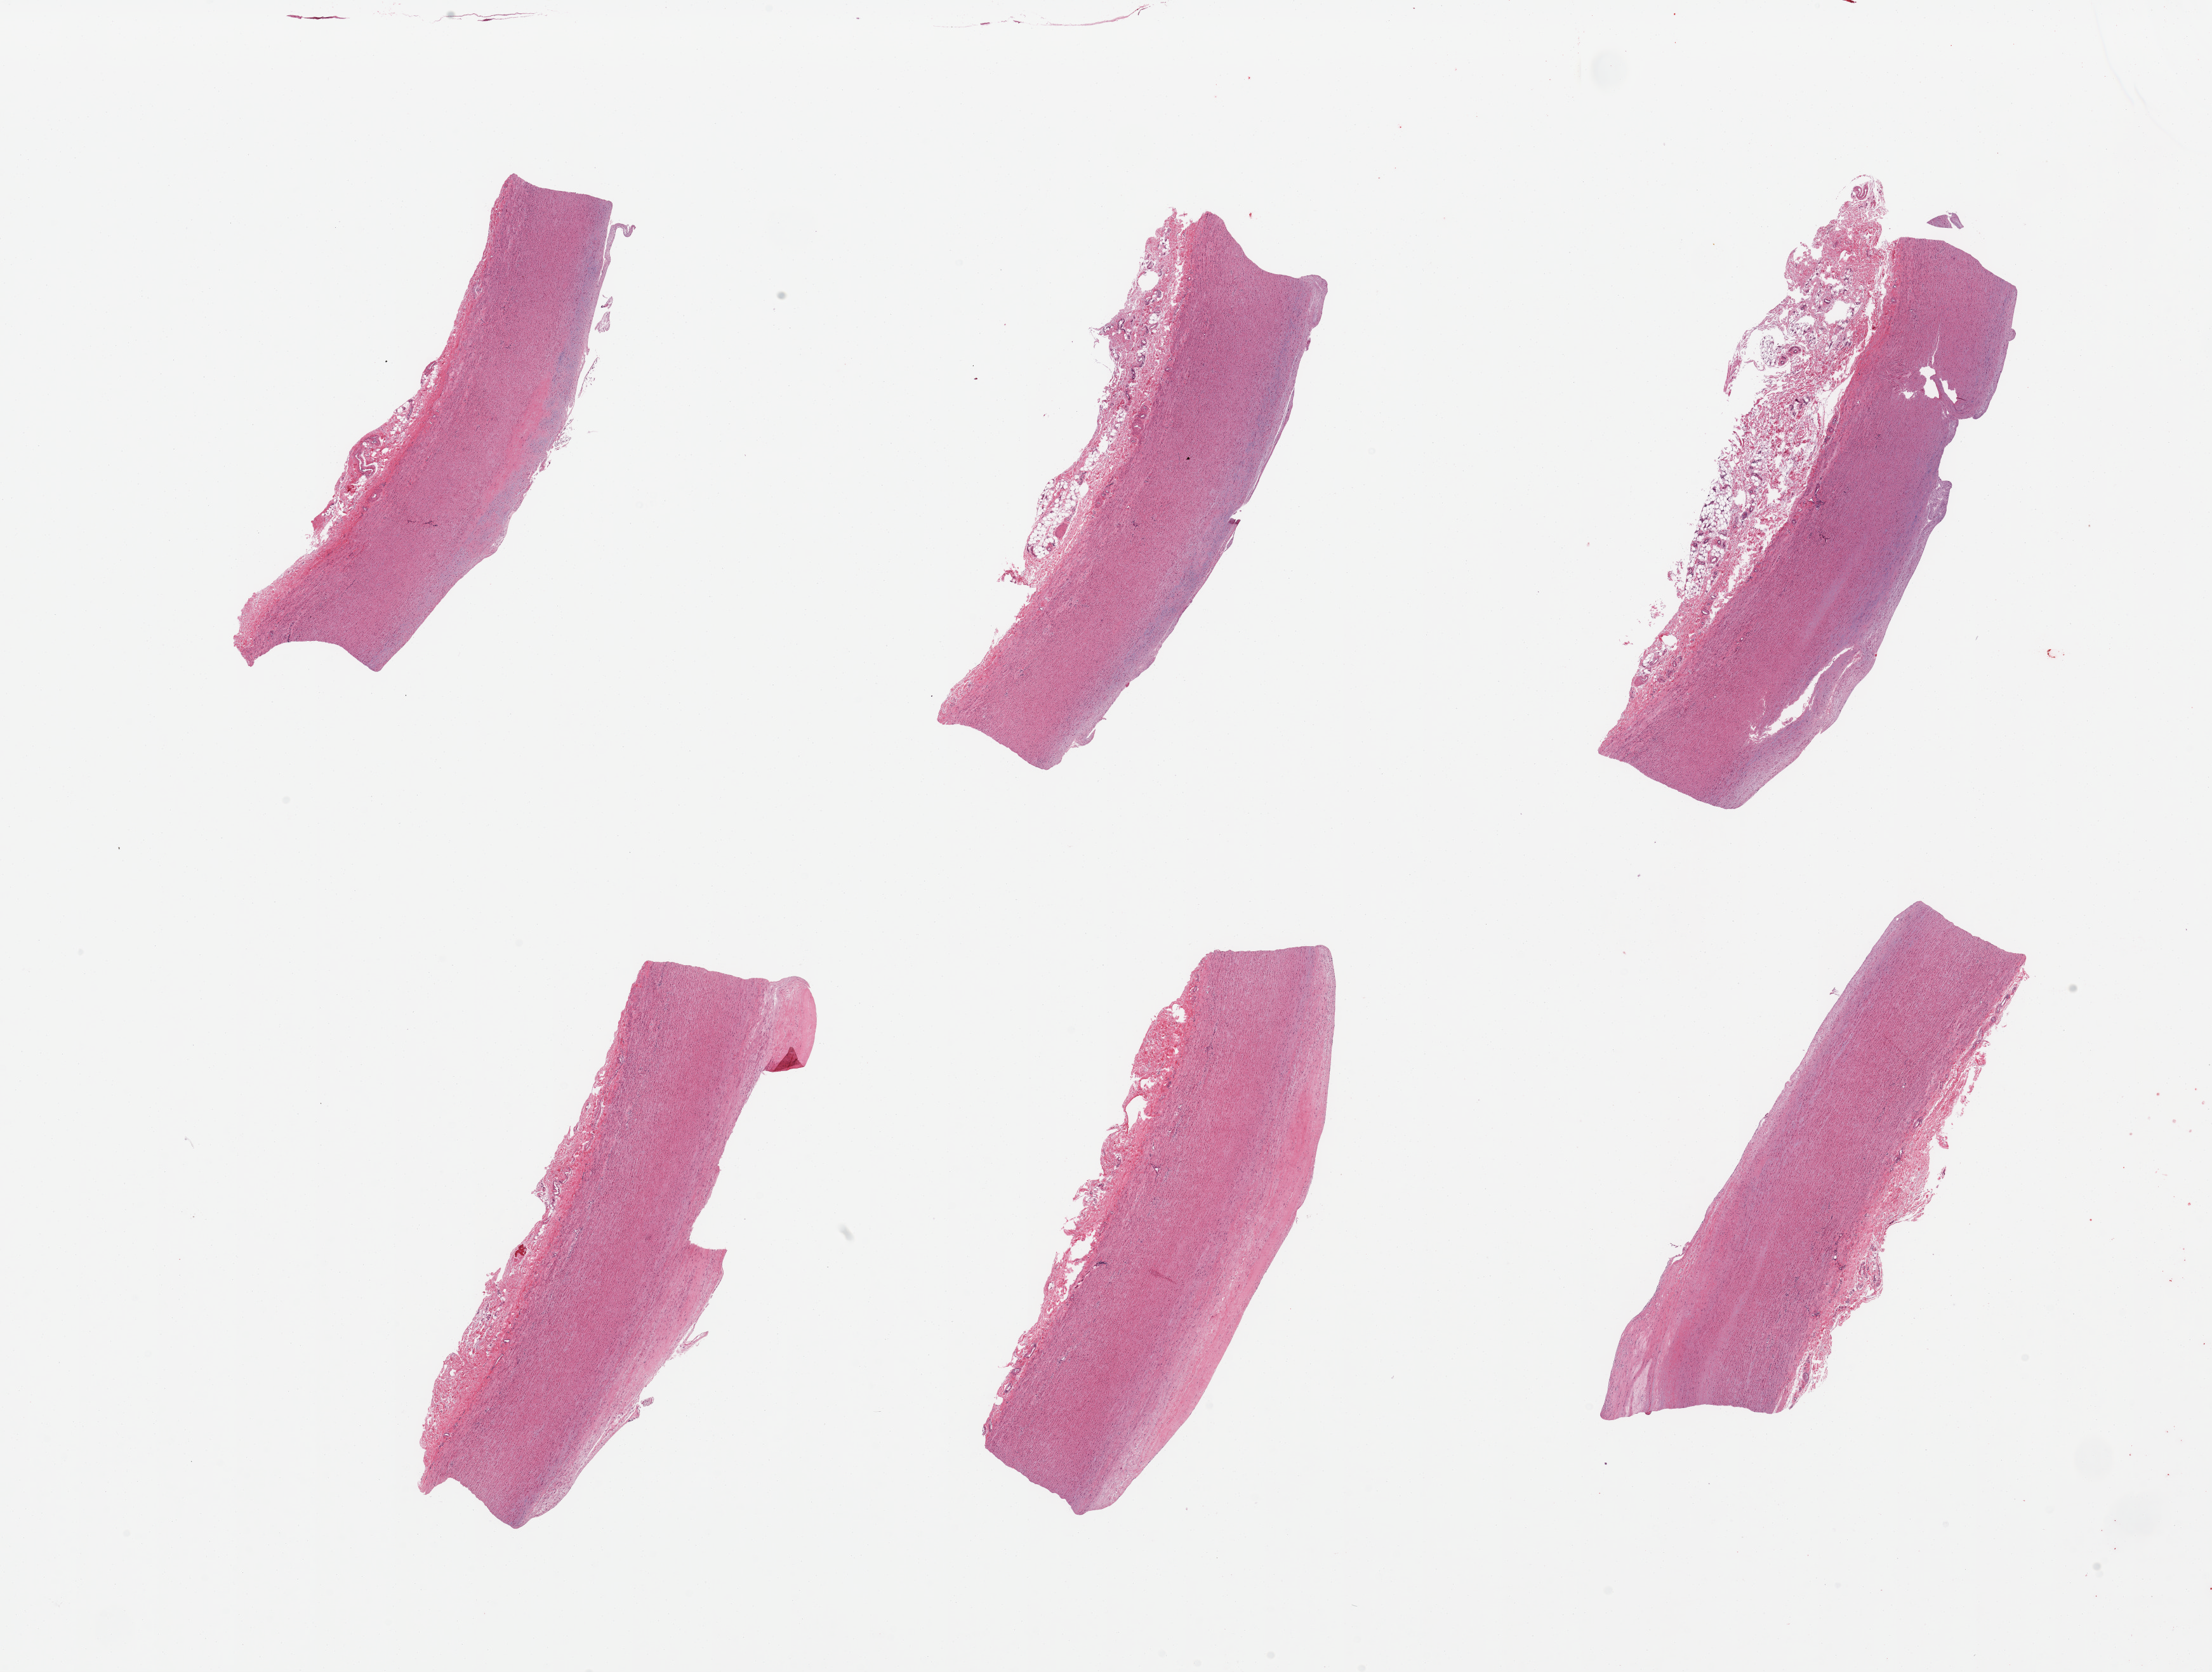
Hematoxylin and eosin (H&E) whole-slide image — whole scanned area (about 27.6 x 20.8 mm, acquisition: 20x scan) shown as a low-resolution overview, PAXgene-fixed, paraffin-embedded tissue, section of aorta (target tissue), donor tissue sample. Donor sex: male.
* reviewer comment on this tissue sample: 6 pieces; atherosclerosis